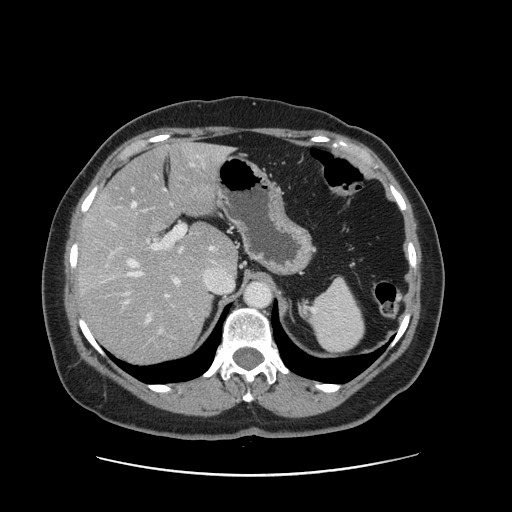
Contrast-enhanced abdominal CT, one axial slice; position 101 of 161 along the scan axis; 120 kVp; intravenous contrast given; soft-tissue window (W 400 / L 40 HU); 2.5 mm slice thickness; 512 × 512 image matrix, field of view 398 × 398 mm. Female patient, age 62 years. From the clinical record (not read from this slice): diagnosis: colorectal cancer liver metastases, imaged before liver resection; multiple liver metastases: no; largest metastasis: 2.5 cm; disease in both lobes: no.
Outlined on this slice (manually delineated by an expert):
- hepatic veins: bounding box <126,163,233,321> (left, top, right, bottom; pixels)
- liver: <80,144,236,363>
- planned liver remnant (the part of the liver to remain after resection): <103,143,236,271>
- portal vein (with intrahepatic branches): <122,189,186,334>